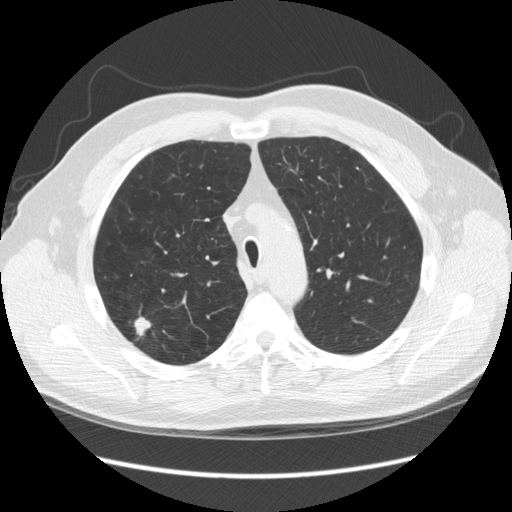
Axial slice from a low-dose chest CT screening exam; third annual screen; lung window (W 1500 / L -600 HU); standard (soft-tissue) reconstruction kernel (STANDARD); slice 62 of 248 in the series; 512 × 512 image matrix. Male, age 64 years at enrolment. Former smoker at enrolment.
Expert-annotated lung lesion, box from (x=118, y=313) to (x=169, y=355) px. The screening reader recorded 4 non-calcified nodules or masses ≥4 mm on this exam; which of them this box marks is not recorded. Later outcome: lung cancer diagnosed 15 days after this screen — adenocarcinoma, NOS, right upper lobe, moderately differentiated (G2), stage IA (AJCC 6th edition), 14 mm at pathology.